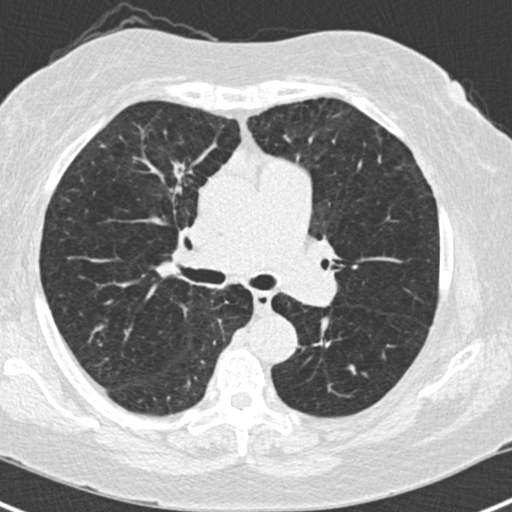
Low-dose screening chest CT, one axial slice; position 92 of 168 along the scan axis; reconstruction kernel B30f; lung window (W 1500 / L -600 HU); 2 mm slice thickness; 512 × 512 image matrix, field of view 303 × 303 mm.
Structures marked on this image (outlined manually by an expert reader):
- lesion 1 (tumor, upper lobe of right lung): bounding box [x1, y1, x2, y2] px = [173, 163, 185, 182]